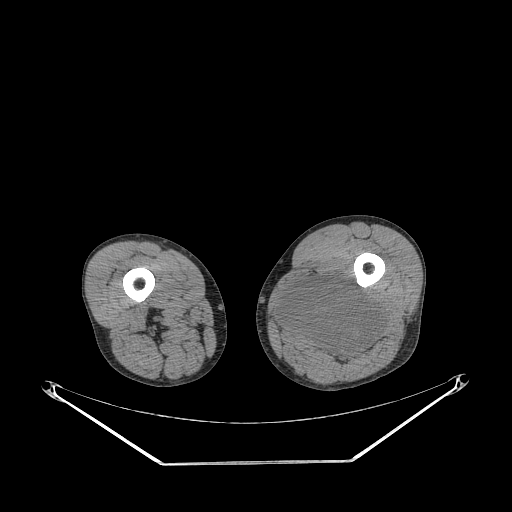
CT of an extremity soft-tissue mass (from a PET/CT study), one axial slice. Position 227 of 267 along the scan axis. 140 kVp. Soft-tissue window (W 400 / L 40 HU). 3.75 mm slice thickness. 512 × 512 image matrix, field of view 500 × 500 mm. Male patient. From the clinical record (not read from this slice): histological type: undifferentiated pleomorphic liposarcoma; grade: high; site of the primary tumour: left thigh.
Annotated regions visible in this slice (expert contour drawn on MRI and transferred to this co-registered scan by the dataset authors):
- gross tumour volume including surrounding oedema: bounding box (x1, y1, x2, y2) in pixels: (276, 278, 384, 362)
- gross tumour volume (mass): (276, 278, 384, 362)